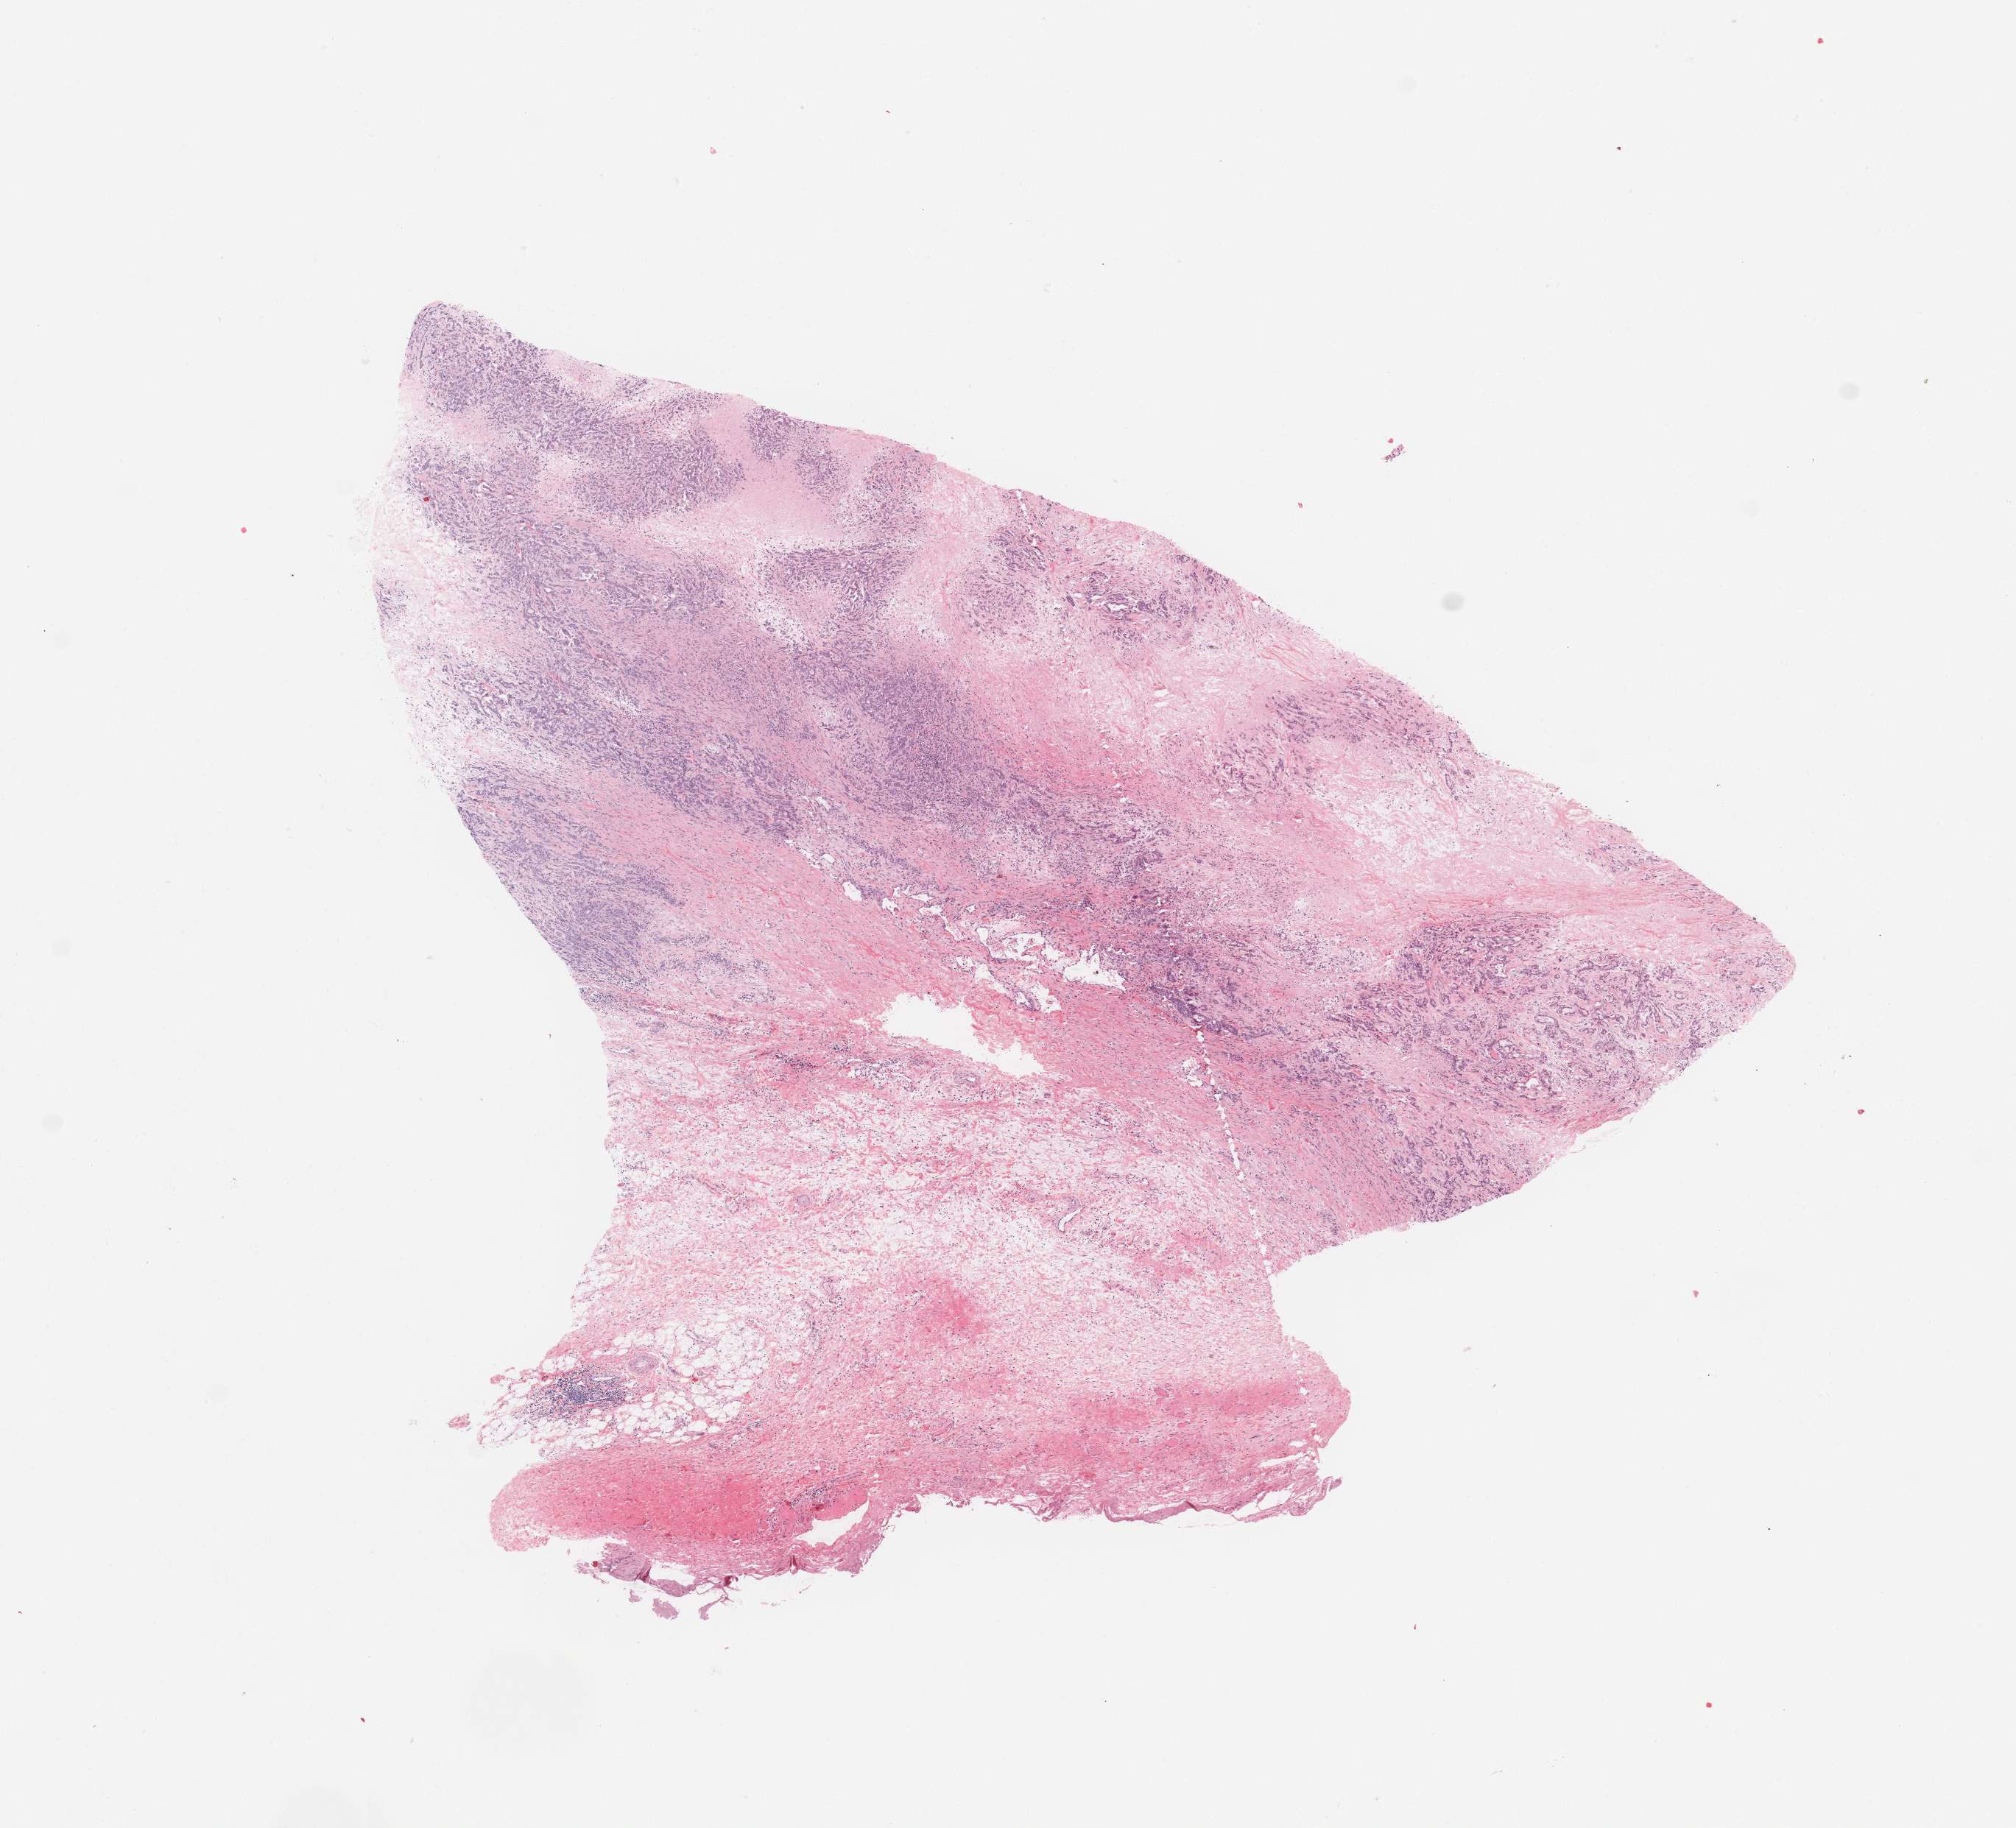
Whole-slide histology image, H&E, whole scanned area (about 10.8 x 9.8 mm) shown as a low-resolution overview; tumour tissue sample, sampled site: pancreas. Patient: female, age 50 years. Histologic grade: G2 (moderately differentiated). Slide review estimates, as recorded: tumour nuclei 60%, necrosis 10%.
- primary tumour site (as recorded): body
- histologic diagnosis: Infiltrating duct carcinoma, NOS
- AJCC pathologic stage: III